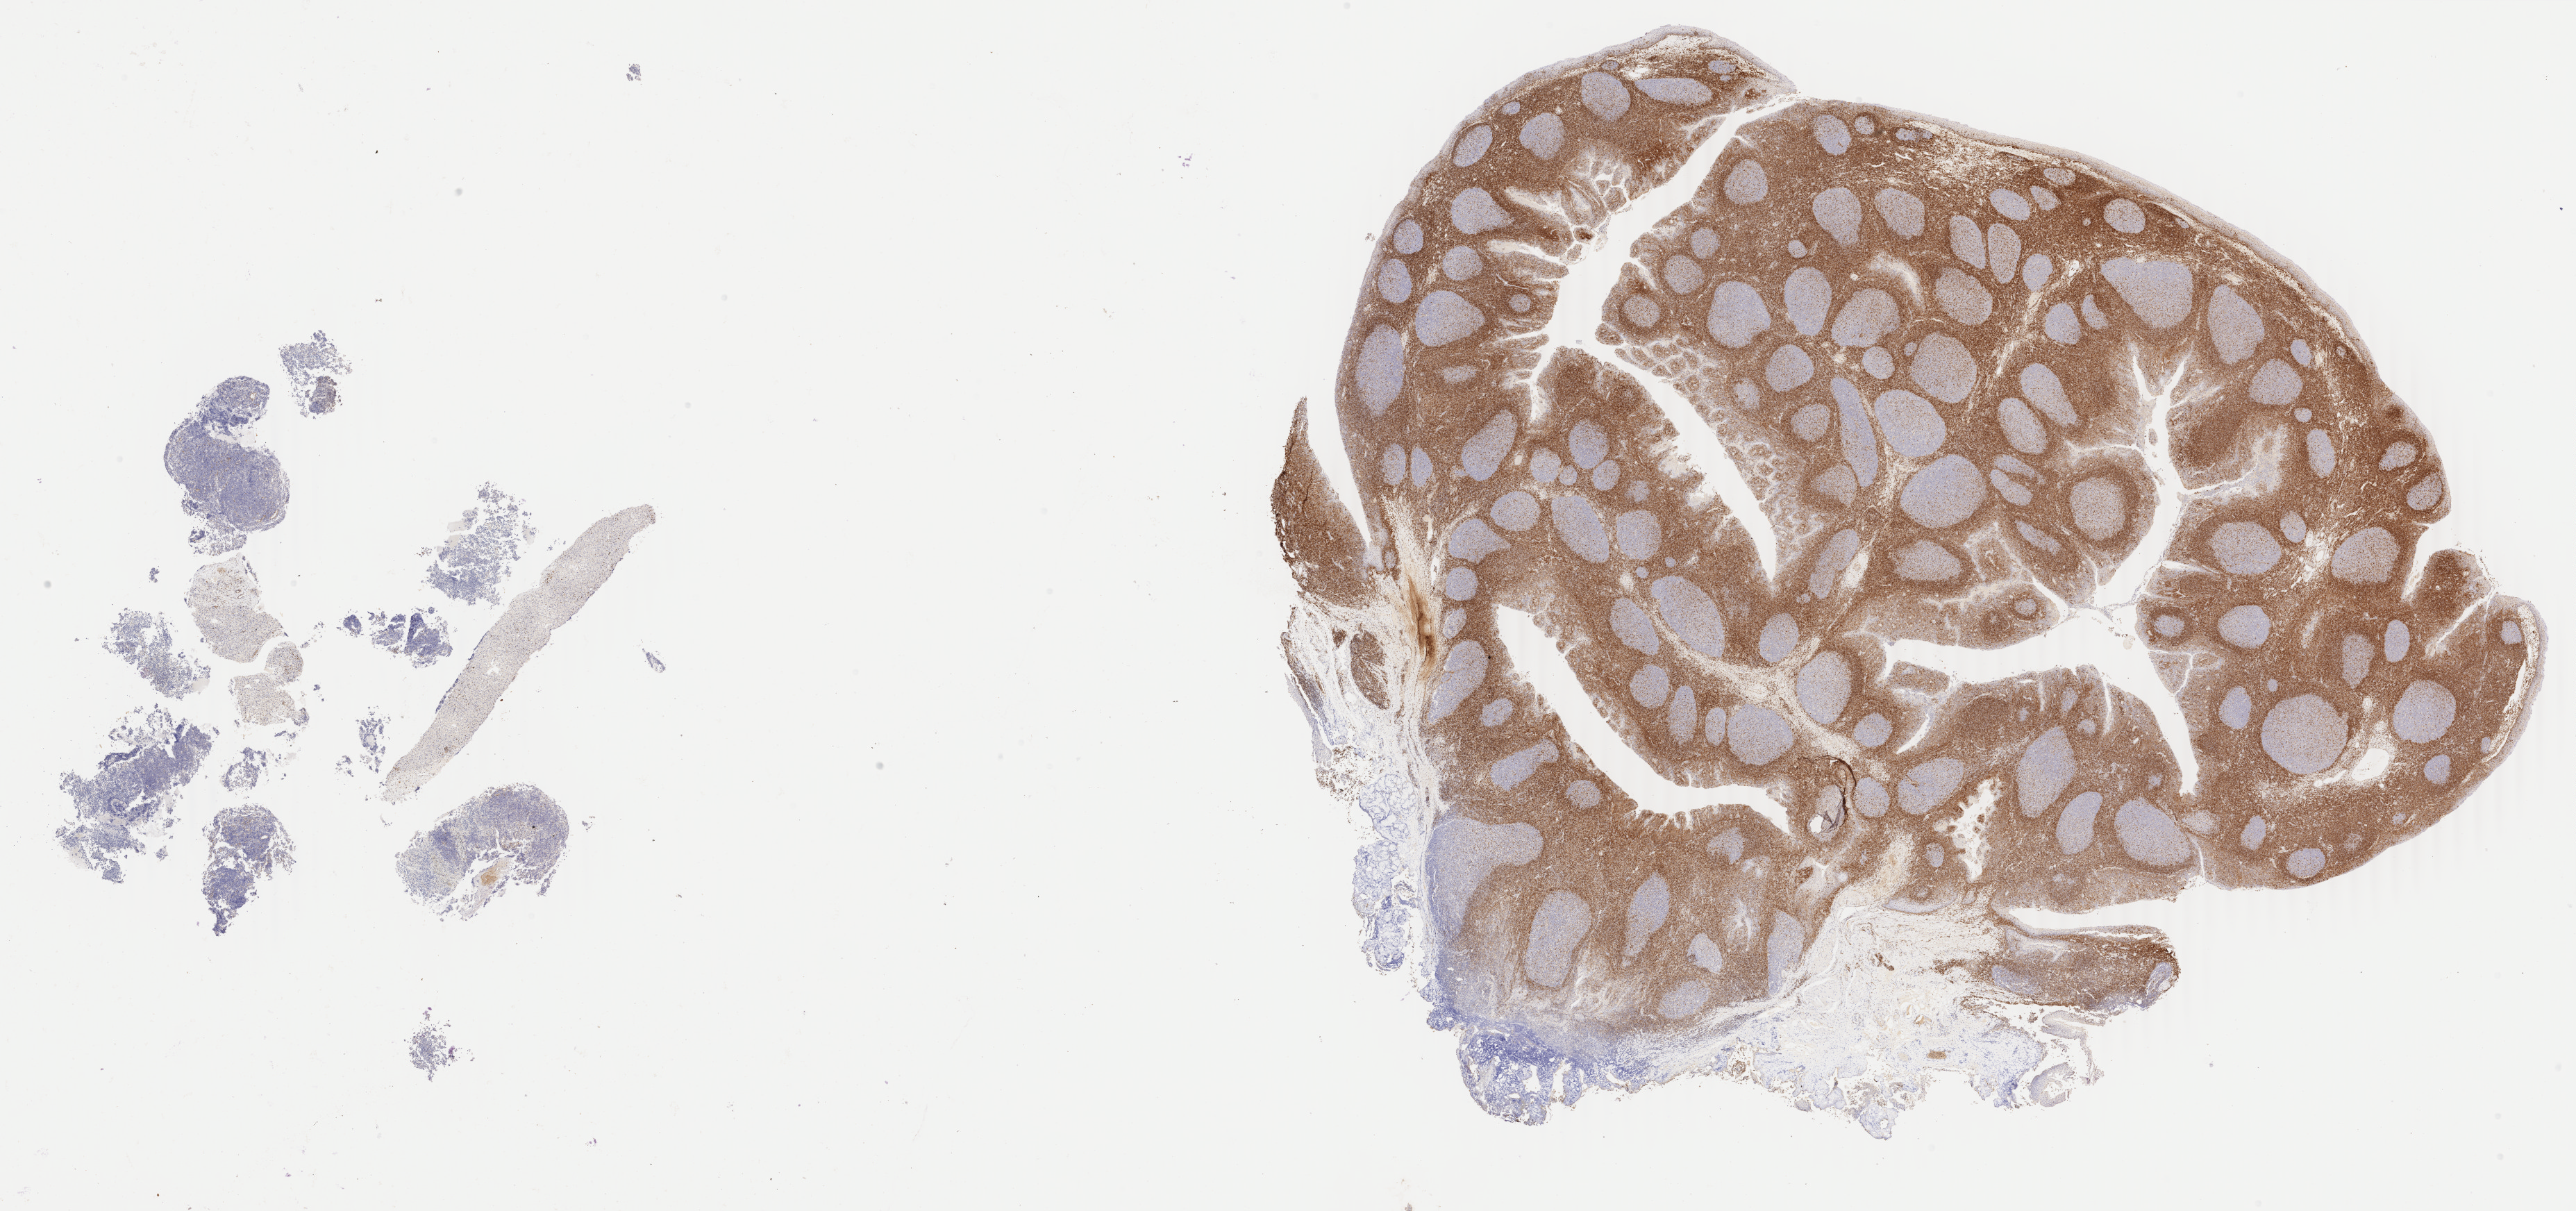
Immunohistochemistry (IHC) whole-slide image stained for BCL2 — a low-resolution overview of the entire scanned area, about 29.5 x 13.9 mm. Tumor tissue. Anatomic site: liver. Patient: male, age at initial diagnosis 5 years.
Diagnosis: Burkitt lymphoma, NOS.